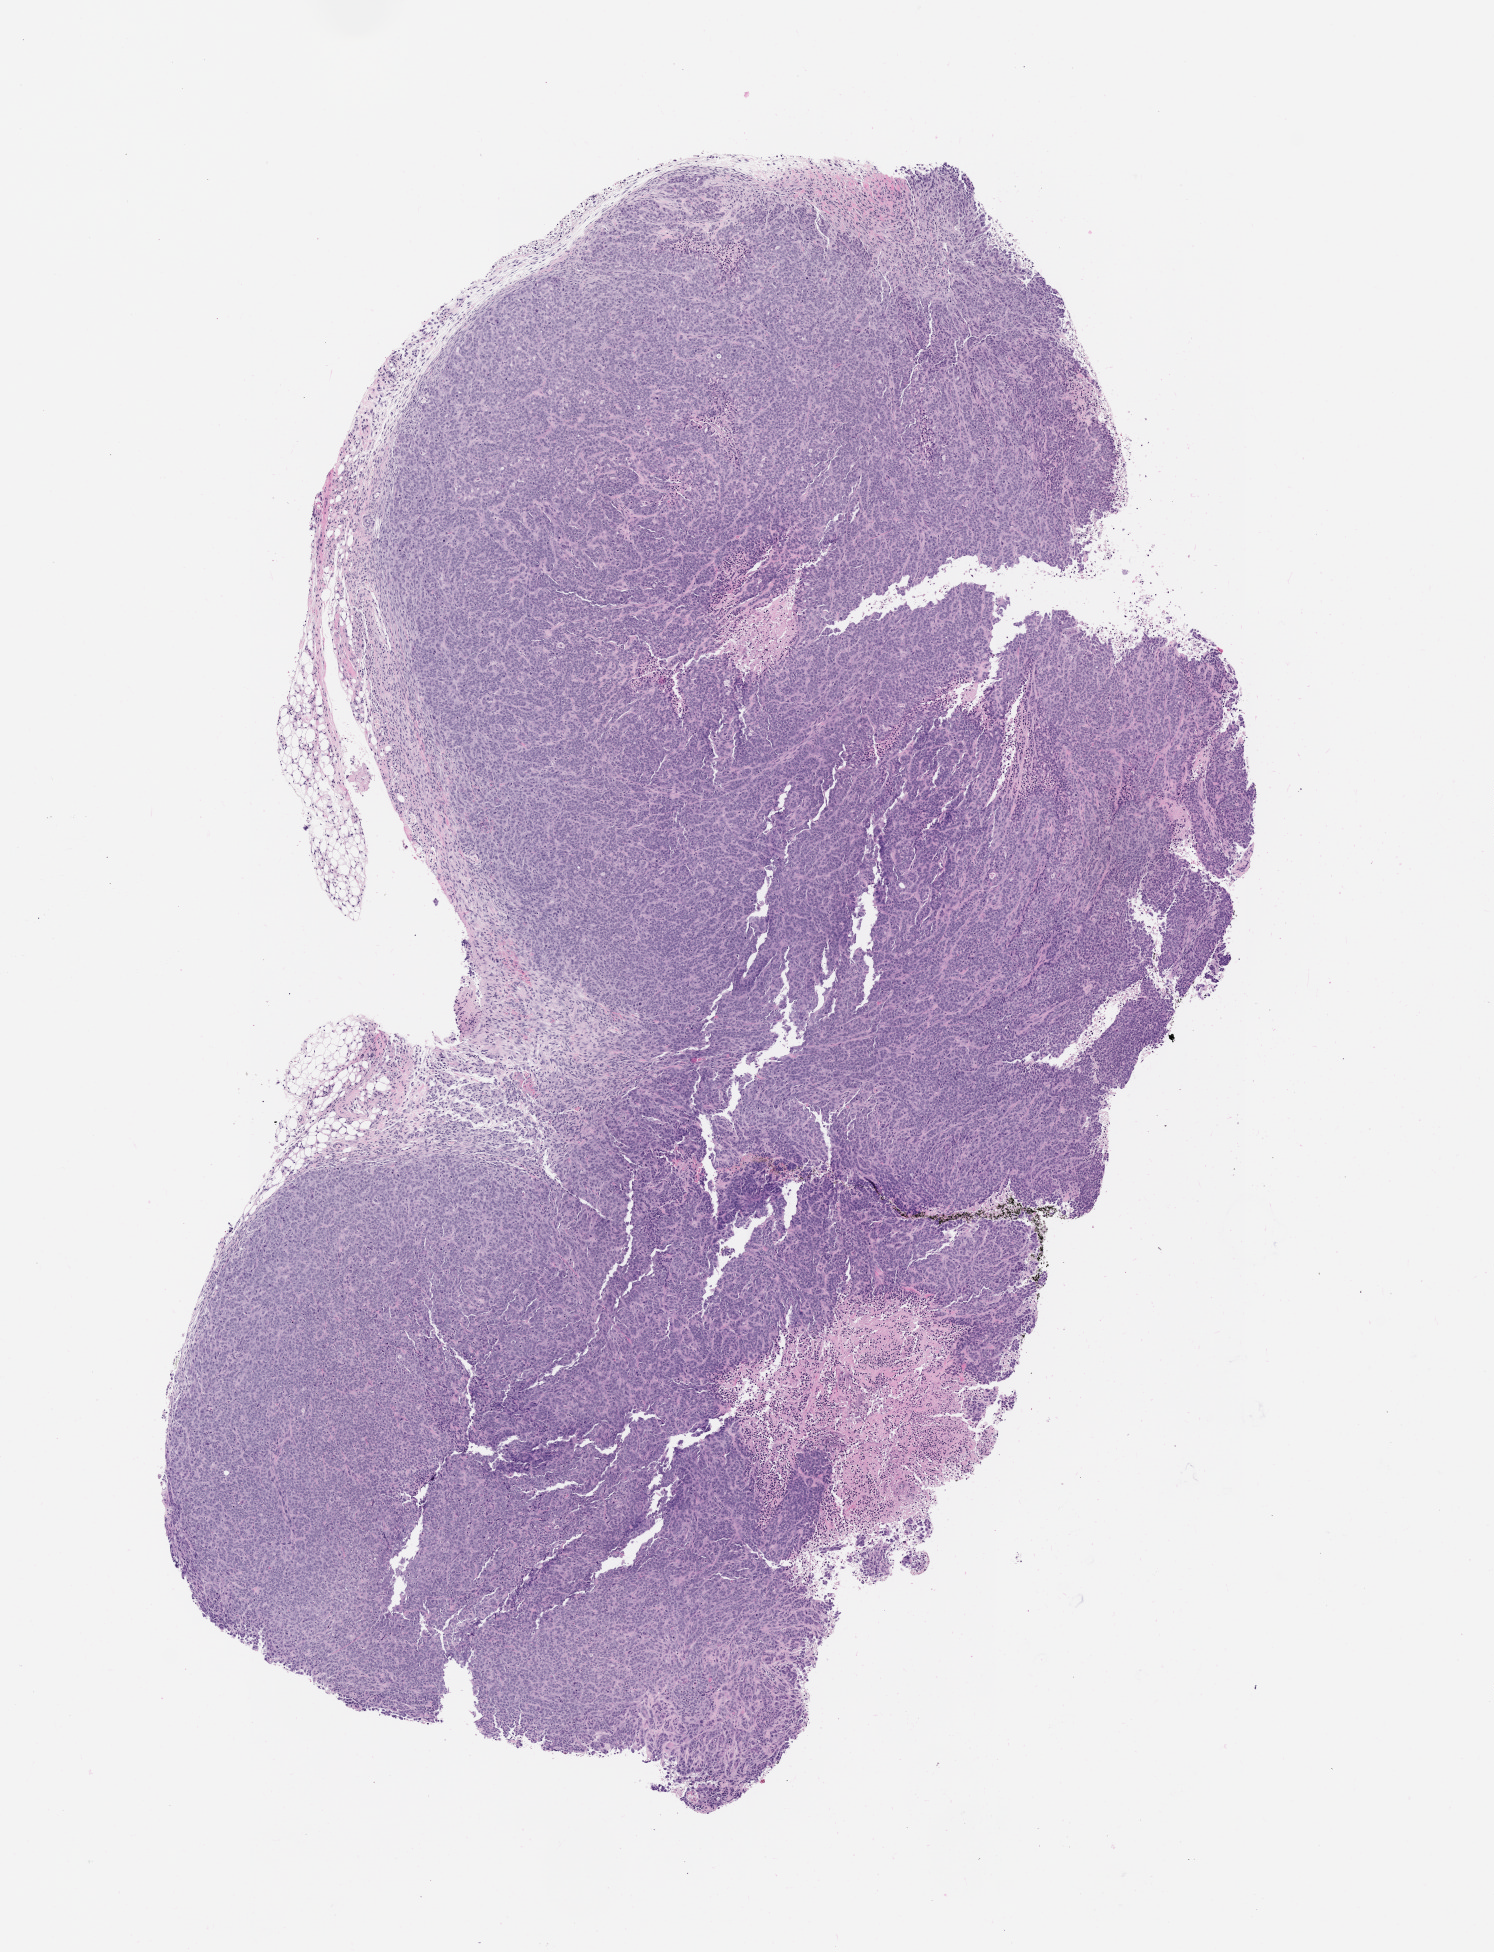
Whole-slide image, haematoxylin and eosin: patient-derived xenograft (human tumor grown in a mouse), passage 0 — shown as a low-resolution overview of the whole scanned area (about 6.0 x 7.9 mm). Formalin-fixed paraffin-embedded section. Tumor site category: pancreas.
Originating patient diagnosis: Pancreatic Adenocarcinoma.